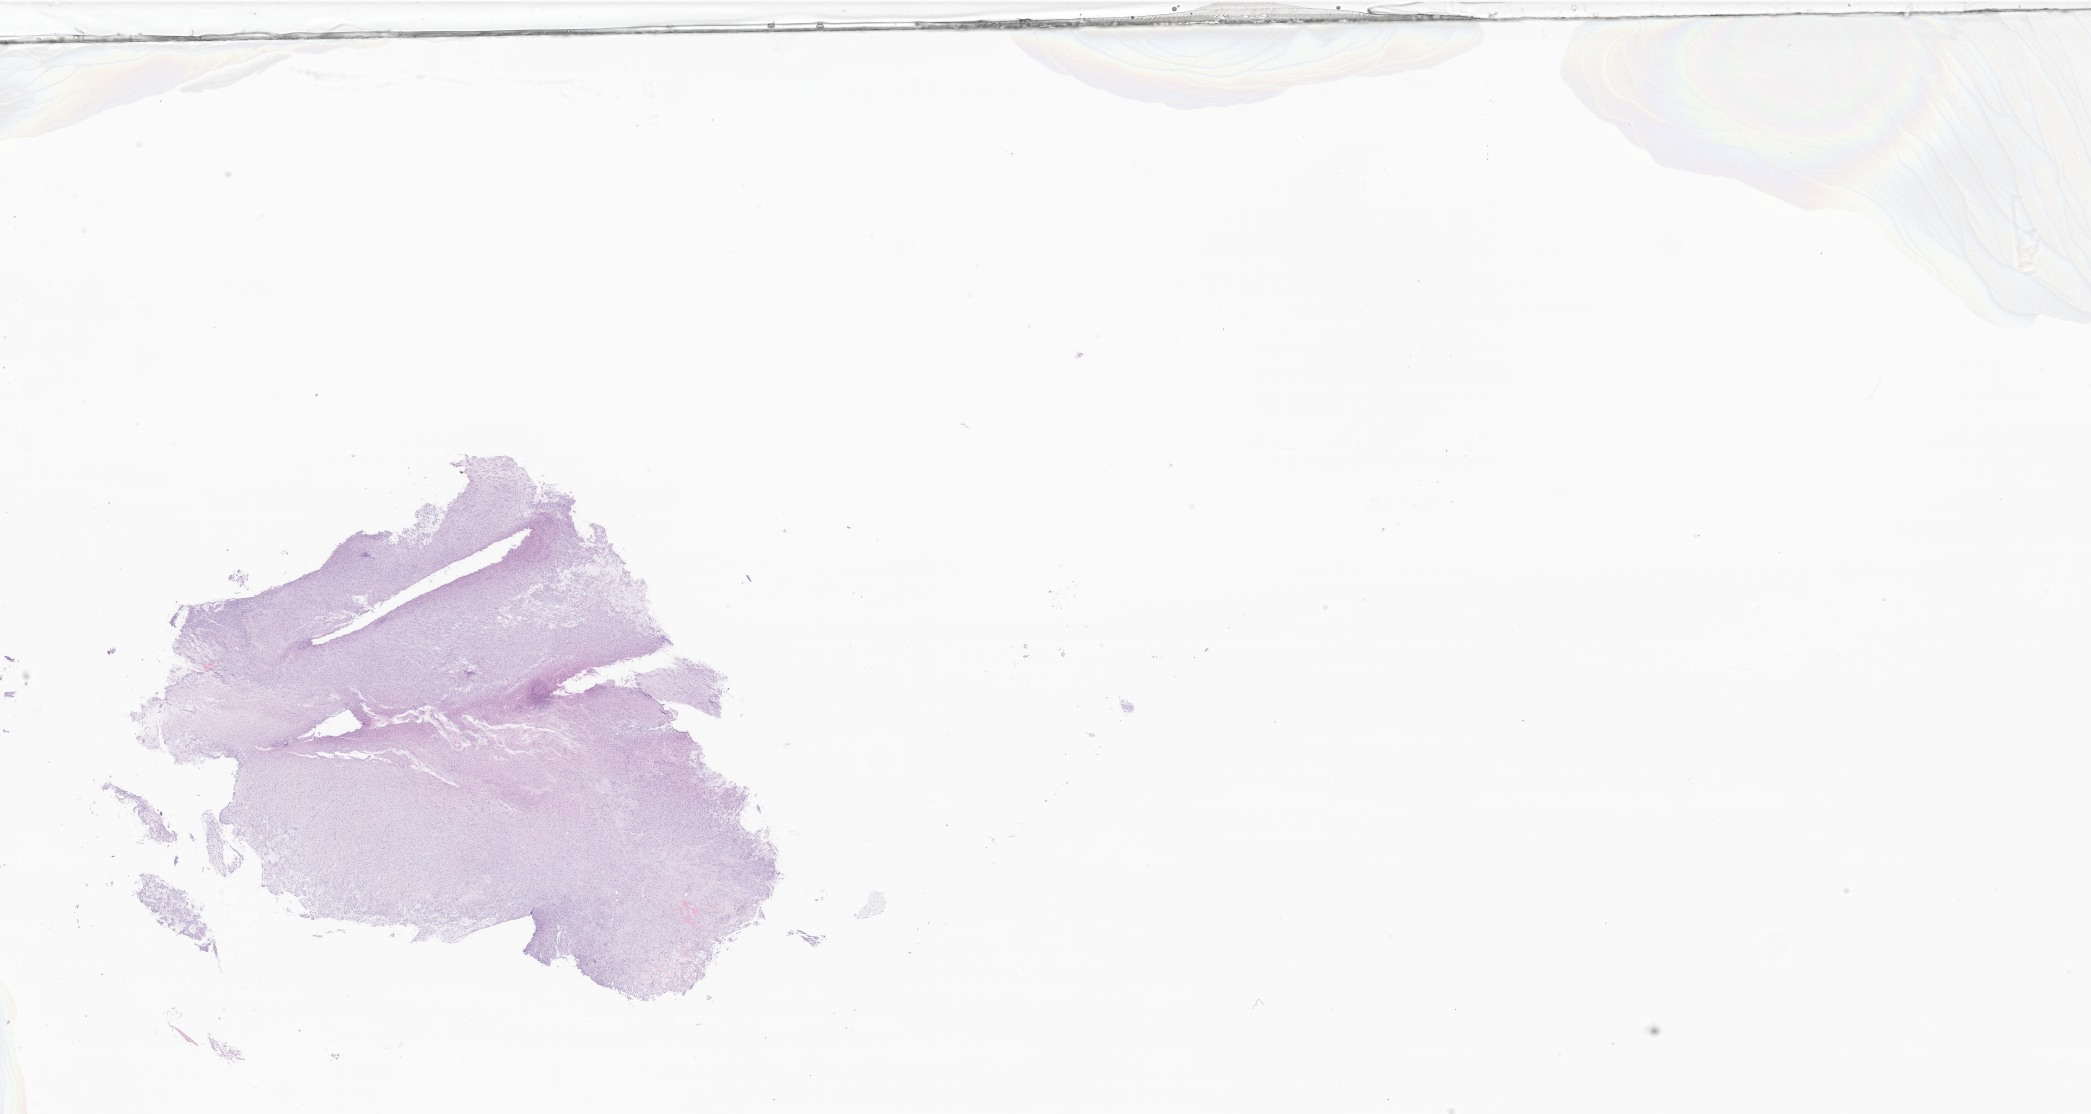
H&E whole-slide image of tumor tissue from the brain, whole scanned area (about 35.3 x 18.8 mm) shown as a low-resolution overview, FFPE section. Female patient, age 168 months (14 years).
Diagnosis (ICD-O-3 morphology term): Neoplasm, benign.